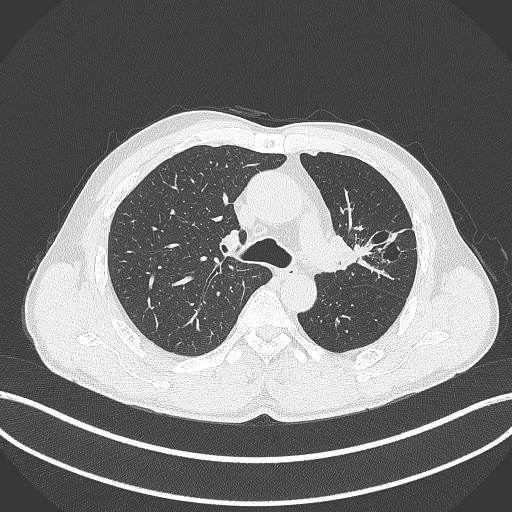
Chest CT, one axial slice. Slice 278 of 429 in the series (ordered by position). 120 kVp. Lung window (W 1500 / L -600 HU). 1 mm slice thickness. 512 × 512 image matrix, field of view 400 × 400 mm. Patient: male, 57 years. Case-level facts recorded for this patient, not image findings: clinical TNM (as recorded): T2b N0 M0.
Outlined on this slice (rectangle marked by the reading radiologist):
- lung tumour (recorded histology: squamous cell carcinoma): bounding box [x1, y1, x2, y2] px = [331, 230, 389, 276]